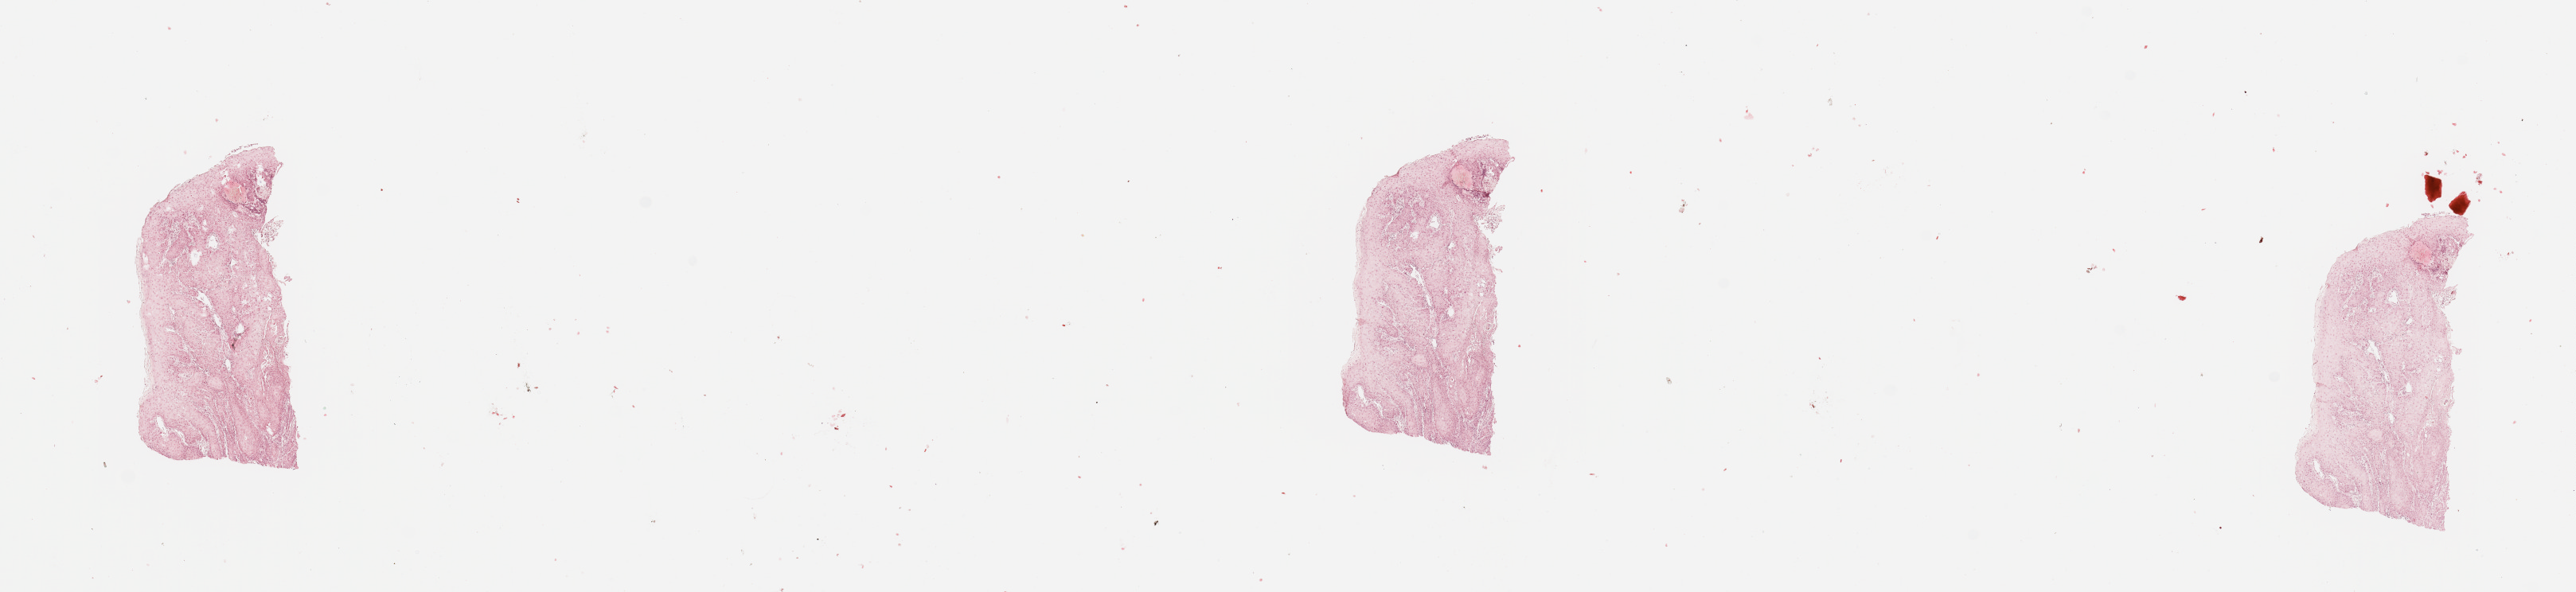
Whole-slide histology image, H&E — low-resolution overview of the scanned area, about 25.6 x 5.9 mm (from a 20x scan); head and neck, tissue type not recorded. 68-year-old male patient.
Patient diagnosis: Squamous cell carcinoma, NOS (larynx, NOS).